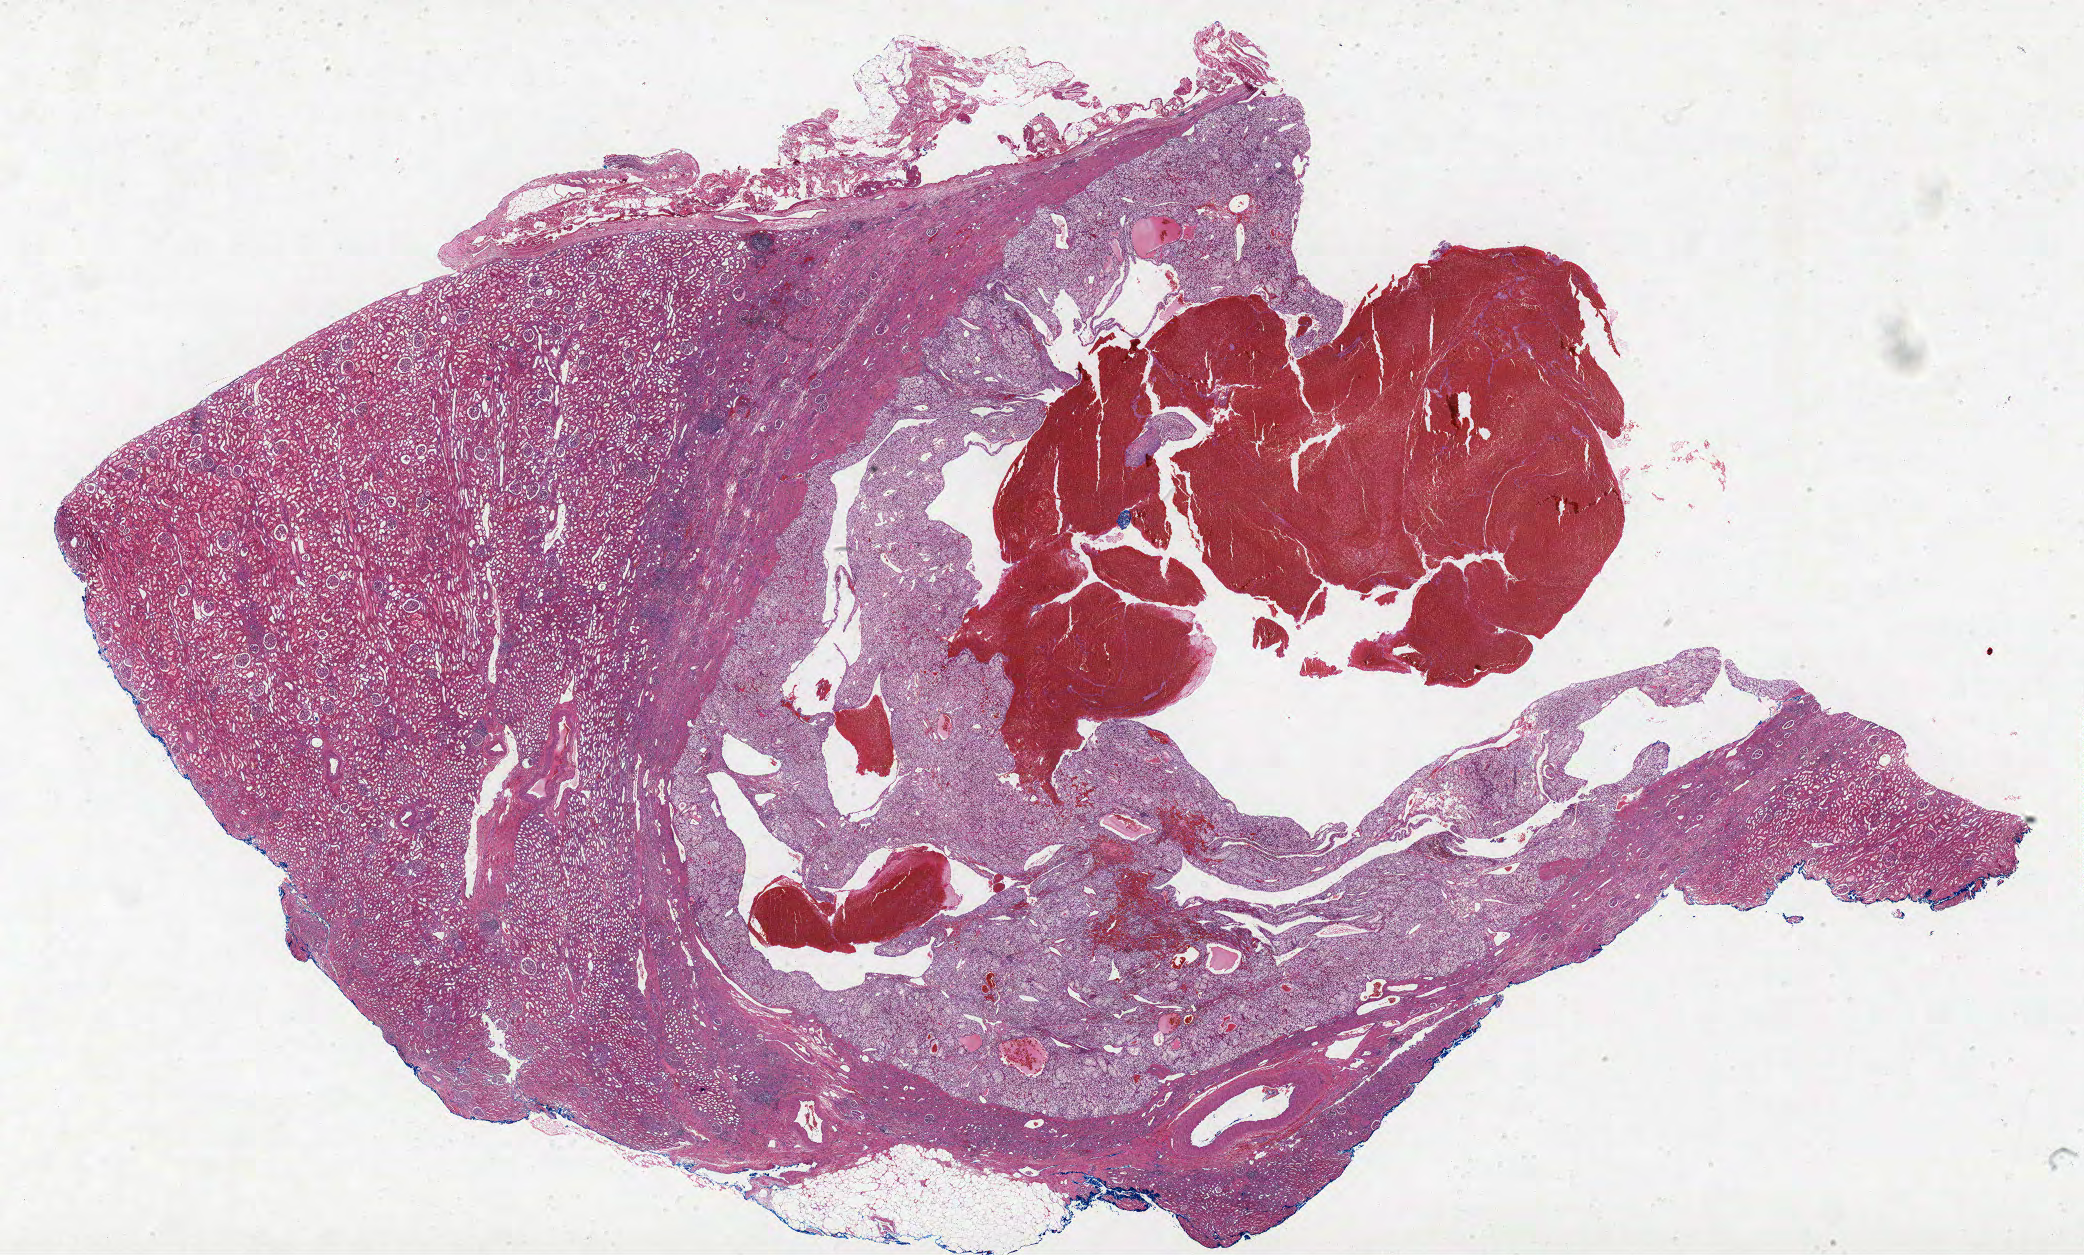
Digitized H&E-stained tissue section (whole slide) — a low-resolution overview of the entire scanned area, about 33.3 x 20.1 mm (from a 40x scan). FFPE section. Sample: primary tumour, kidney. Female, age 55 years at initial diagnosis. Histologic grade: G2 (moderately differentiated).
* AJCC pathologic stage: I
* pathologic diagnosis: Clear cell adenocarcinoma, NOS